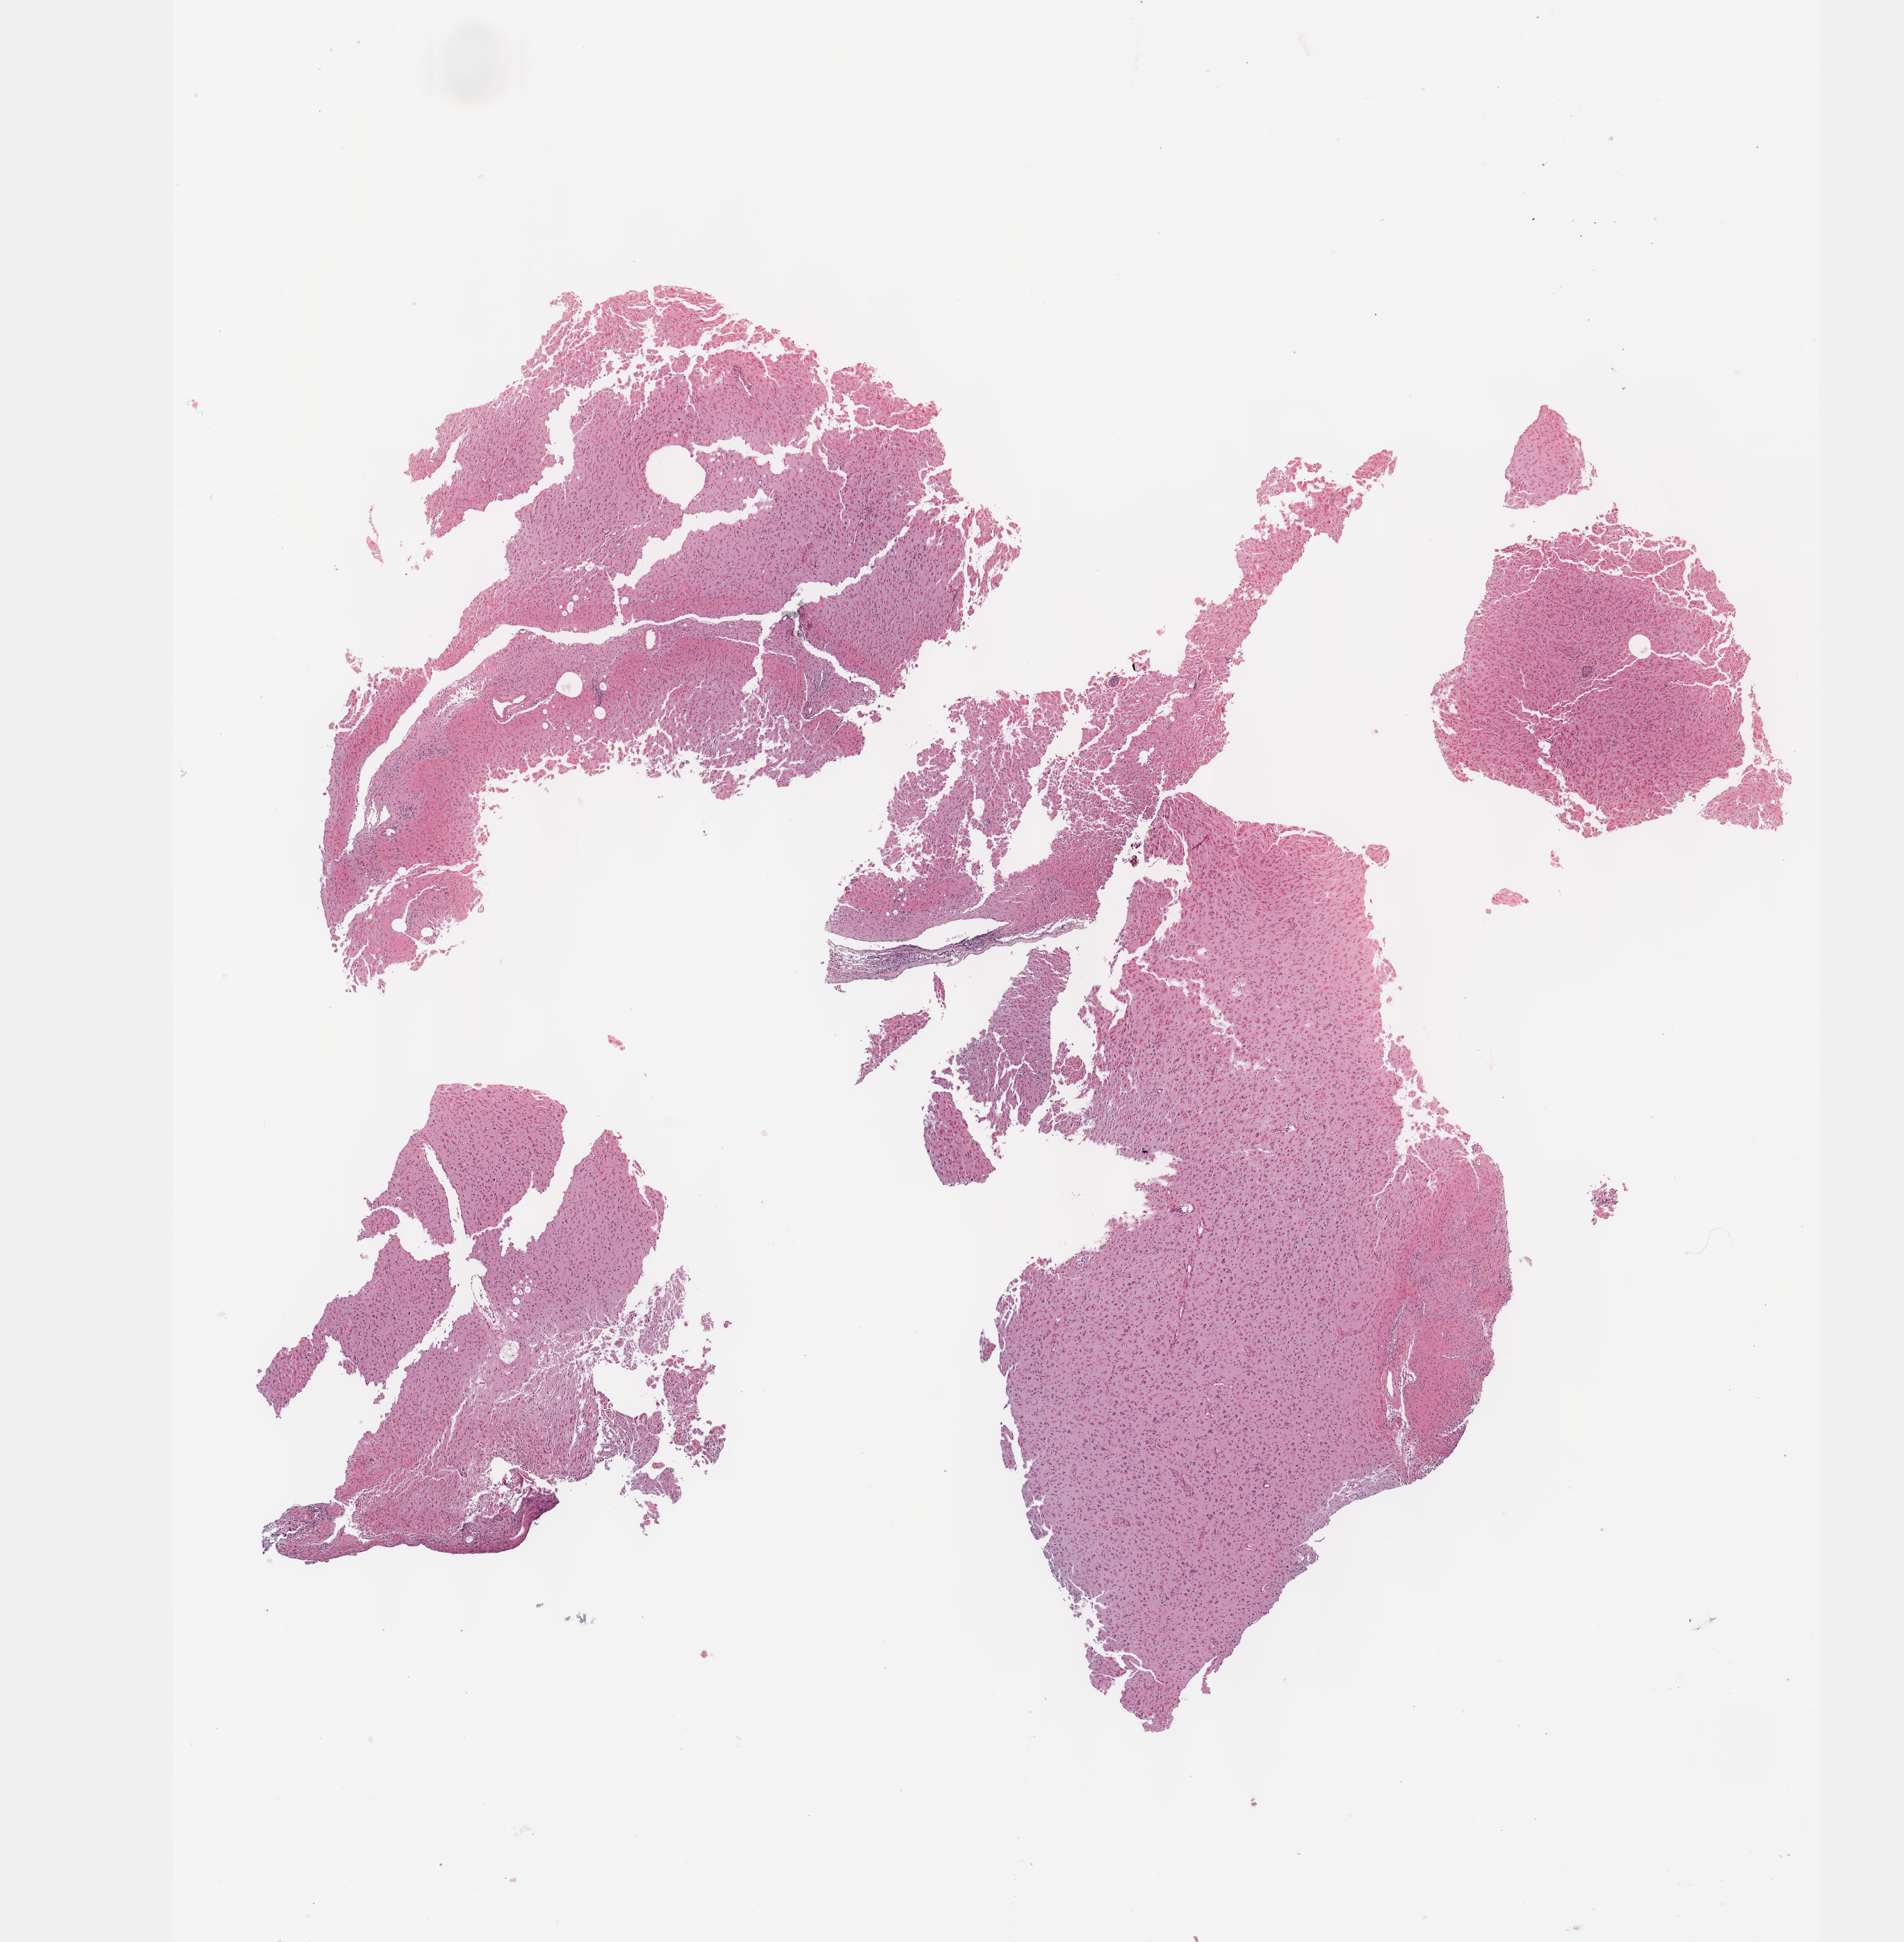
Digitized Hematoxylin and eosin (H&E) stained tissue section (whole slide), low-resolution overview of the scanned area, about 11.1 x 11.3 mm (acquisition: 40x scan), formalin-fixed paraffin-embedded (FFPE) diagnostic section, primary tumour sample from the brain. Female patient; age at initial diagnosis 74 years. Histologic grade: G3 (poorly differentiated).
Diagnosis: Astrocytoma, anaplastic.